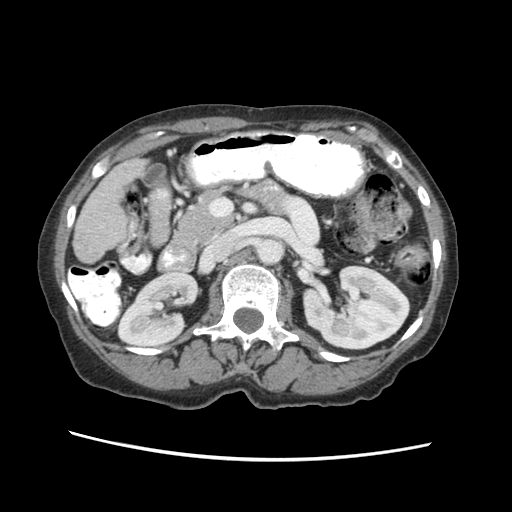
Contrast-enhanced abdominal CT (liver protocol), one axial slice. Slice 14 of 63 in the series (ordered by position). Soft-tissue window (W 400 / L 40 HU). 2.5 mm slice thickness. 512 × 512 image matrix. Case-level facts recorded for this patient, not image findings: diagnosis: hepatocellular carcinoma (patient treated with transarterial chemoembolisation; whether this scan precedes or follows treatment is not stated here); TNM stage (as recorded): Stage-I; Child-Pugh class: B; tumour differentiation: well differentiated; tumour nodularity: uninodular.
Annotated regions visible in this slice (semi-automatically segmented with operator editing):
- liver parenchyma outside the tumour (the mass and vessels are separate outlines, so this box may not span the whole liver): bounding box [x1, y1, x2, y2] px = [72, 156, 147, 262]